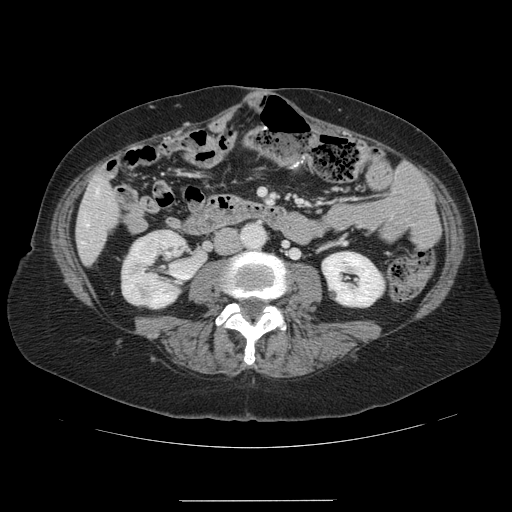
Contrast-enhanced abdominal CT, one axial slice; slice 23 of 141 in the series (ordered by position); 120 kVp; intravenous contrast given; soft-tissue window (W 400 / L 40 HU); 512 × 512 image matrix. Female patient, age 74 years. Case-level facts recorded for this patient, not image findings: diagnosis: colorectal cancer liver metastases, imaged before liver resection; multiple liver metastases: yes; largest metastasis: 7 cm; disease in both lobes: yes.
Outlined on this slice (outlined manually by an expert reader):
- hepatic veins: bounding box (x1, y1, x2, y2) in pixels: (86, 224, 88, 226)
- liver: (77, 178, 117, 264)
- planned liver remnant (the part of the liver to remain after resection): (88, 178, 97, 264)